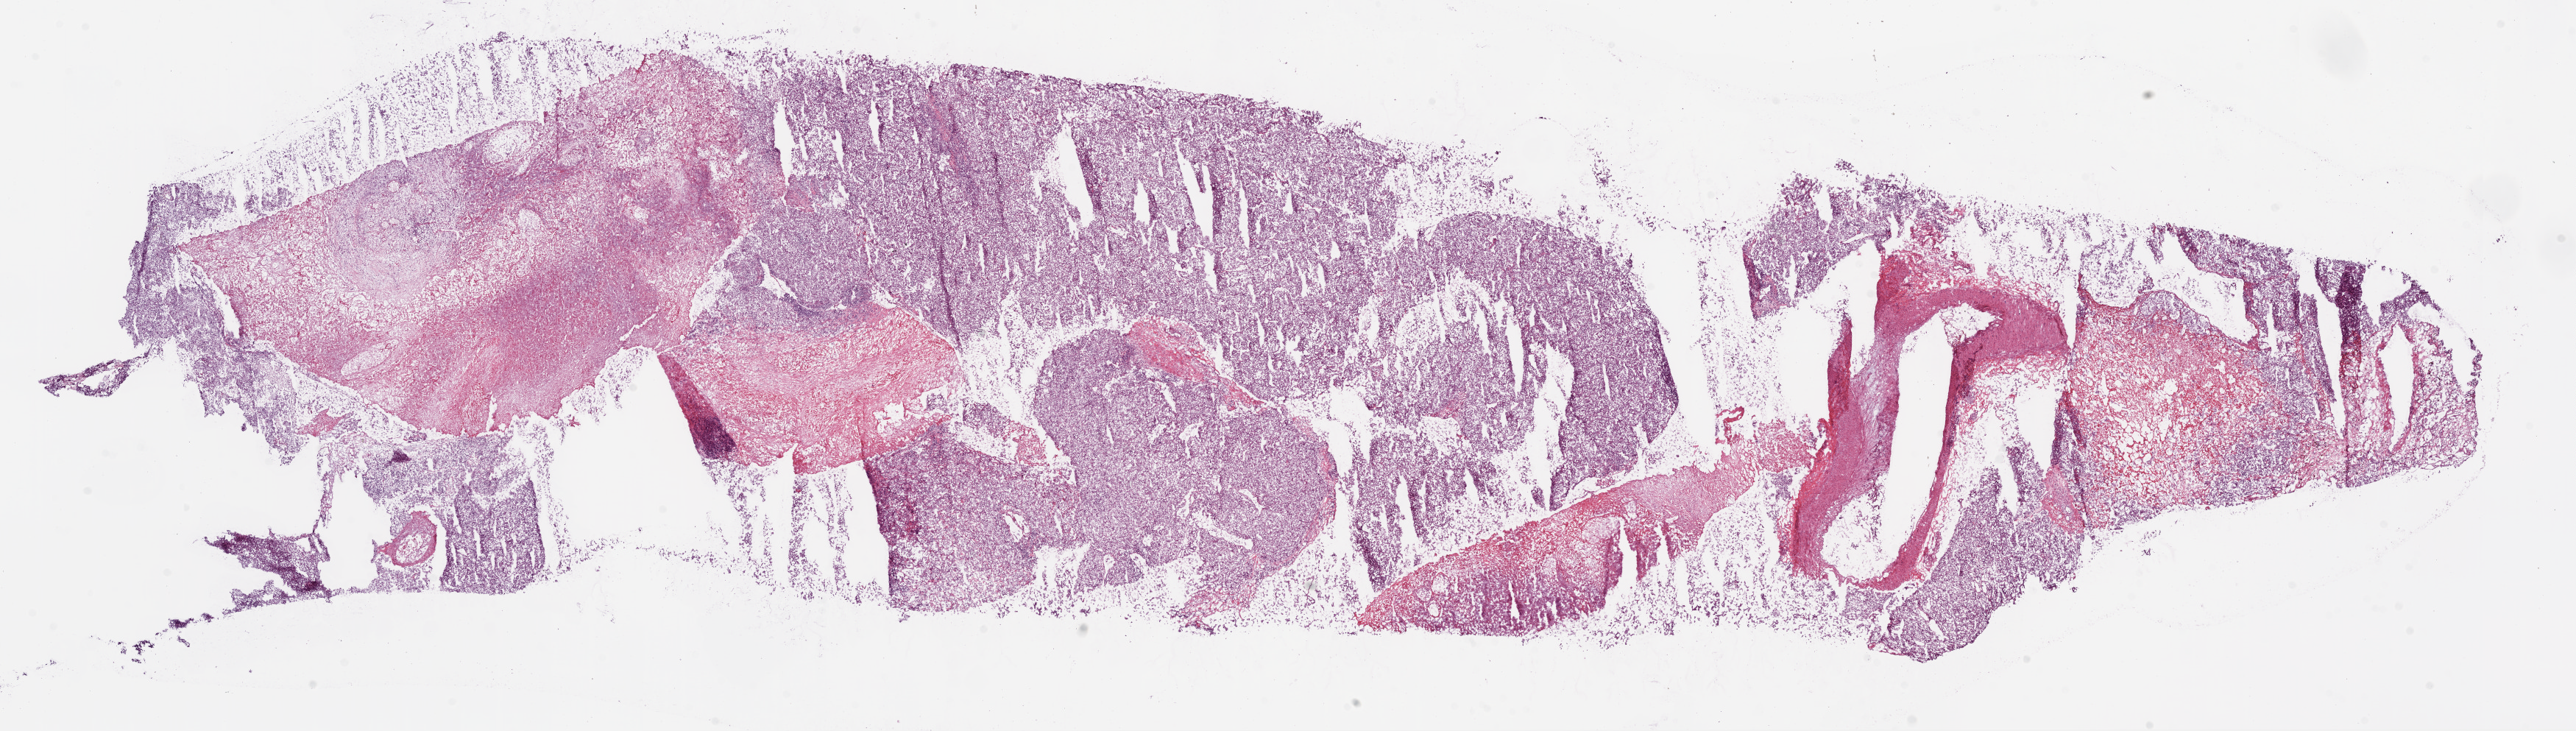
Whole-slide histology image, Hematoxylin and eosin (H&E) stained — shown as a low-resolution overview of the whole scanned area (about 28.1 x 8.0 mm, from a 20x scan); frozen section from the bottom of the tissue portion; sample: primary tumour, kidney. Male, age 59 years at initial diagnosis. Histologic grade: G4 (undifferentiated). Composition of this section per pathologist review: tumour cells 65%, tumour nuclei 85%, normal cells 0%, stromal cells 10%, necrosis 25%.
- pathologic diagnosis: Clear cell adenocarcinoma, NOS
- AJCC pathologic stage: IV